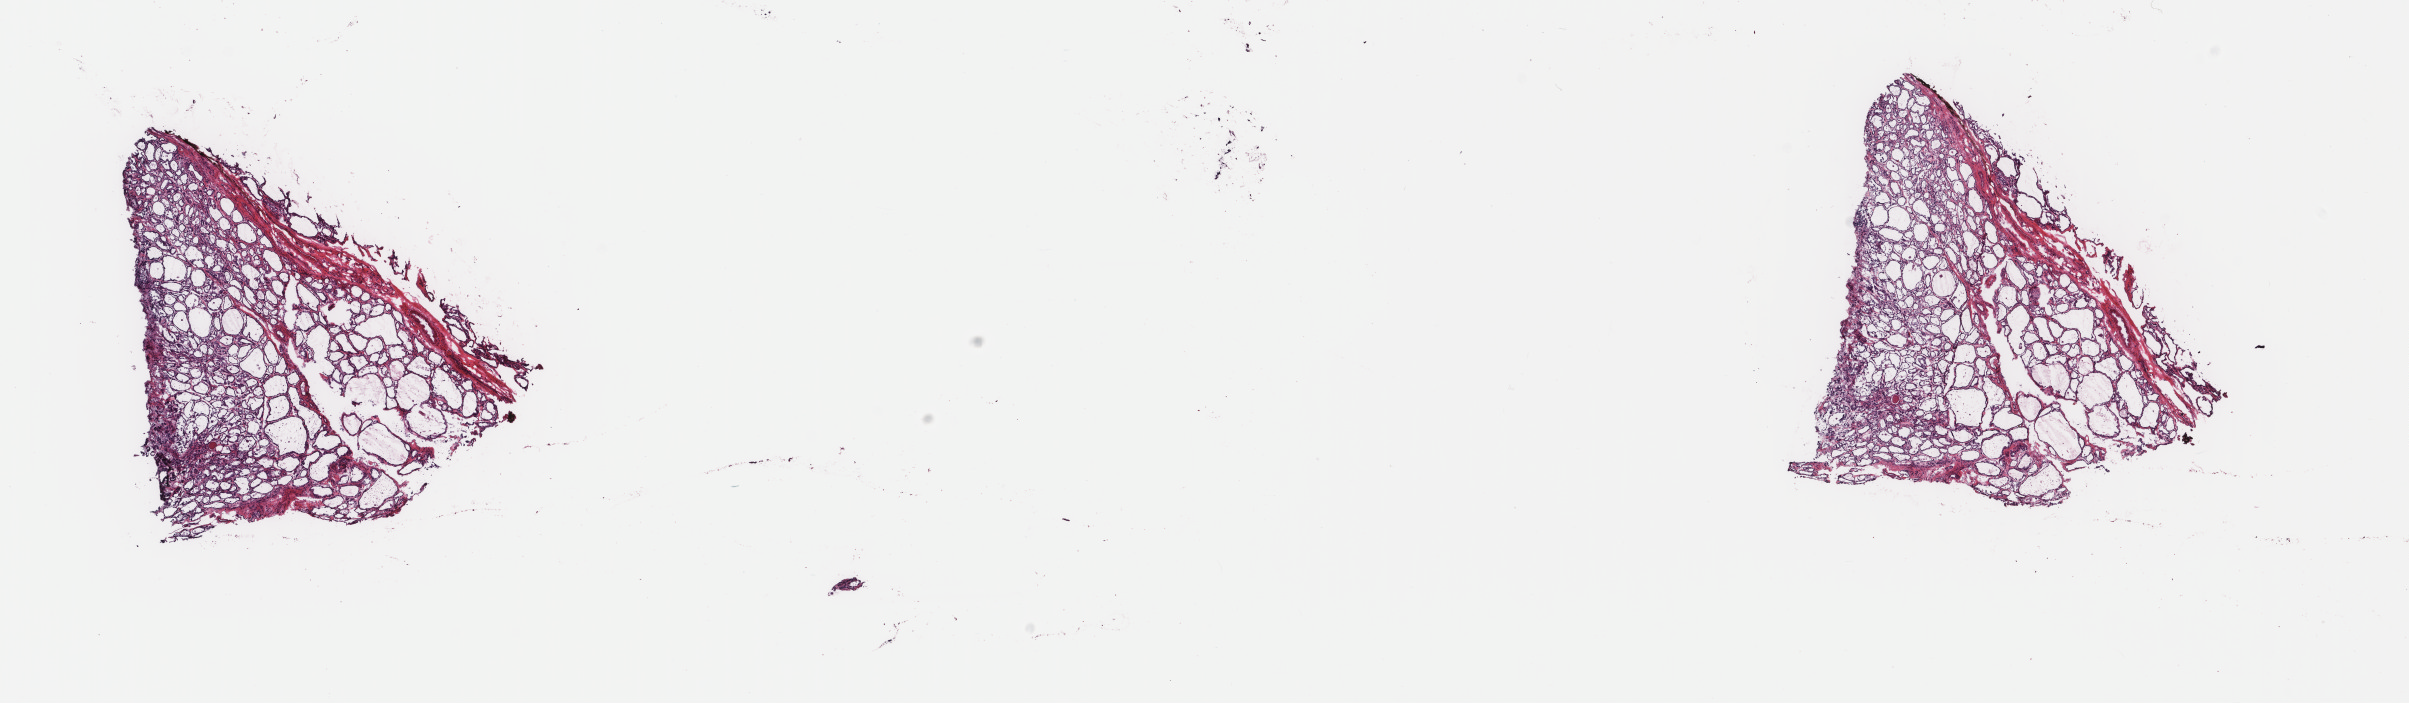
Digitized H&E-stained tissue section (whole slide) — shown as a low-resolution overview of the whole scanned area (about 19.1 x 5.6 mm); frozen section from the top of the tissue portion; sample: primary tumour, thyroid. Female patient. Slide review estimates, as recorded: tumour cells 85%, tumour nuclei 85%, normal cells 0%, stromal cells 15%, necrosis 0%. Inflammatory infiltration, as recorded: lymphocyte infiltration 2%, monocyte infiltration 0%, neutrophil infiltration 0%.
TNM: T2 N1a M0. AJCC pathologic stage: III (5th edition). Pathologic diagnosis: Papillary adenocarcinoma, NOS.